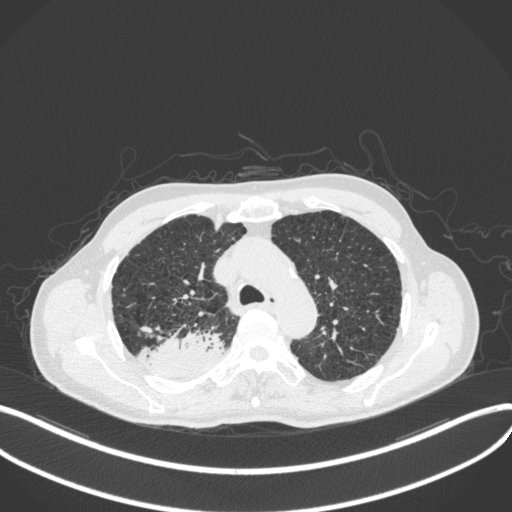
Chest CT, one axial slice. Slice 326 of 423 in the series (ordered by position). Lung window (W 1500 / L -600 HU). 1 mm slice thickness. 512 × 512 image matrix, field of view 400 × 400 mm. Male patient, age 79 years. Case-level facts recorded for this patient, not image findings: clinical TNM (as recorded): T3 N0 M0.
Structures marked on this image (rectangle marked by the reading radiologist):
- lung tumour (recorded histology: adenocarcinoma): bounding box [x1, y1, x2, y2] px = [143, 332, 224, 378]